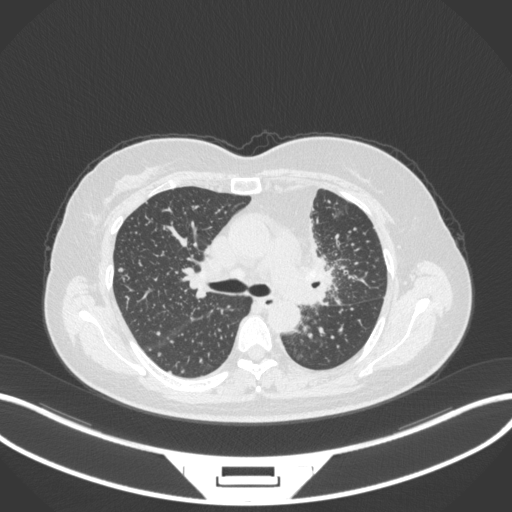
Chest CT, one axial slice; position 212 of 348 along the scan axis; 120 kVp; lung window (W 1500 / L -600 HU); 1 mm slice thickness; 512 × 512 image matrix, field of view 400 × 400 mm. Patient: female, 49 years. Case-level facts recorded for this patient, not image findings: clinical TNM (as recorded): T1c N0 M1.
Outlined on this slice (rectangle marked by the reading radiologist):
- lung tumour (recorded histology: adenocarcinoma): box from (x=289, y=223) to (x=339, y=313) px